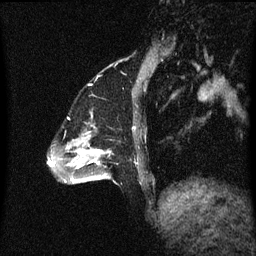
Breast MRI (dynamic contrast-enhanced), one sagittal slice; dynamic contrast-enhanced series, image 2 of 3 at this slice position (ordered by acquisition); 1.5 T; TE 4.2 ms, TR 8.4 ms; 2 mm slice thickness; 256 × 256 image matrix, field of view 200 × 200 mm. Female patient, age 47 years.
Structures marked on this image (semi-automatically segmented with operator editing):
- analysis volume of interest (the breast-tissue region the enhancement analysis was run in; not a lesion): bounding box [x1, y1, x2, y2] px = [85, 136, 117, 183]
- tumour enhancement mask (voxels above the 70 % enhancement threshold inside the analysis volume of interest): [90, 150, 104, 179]